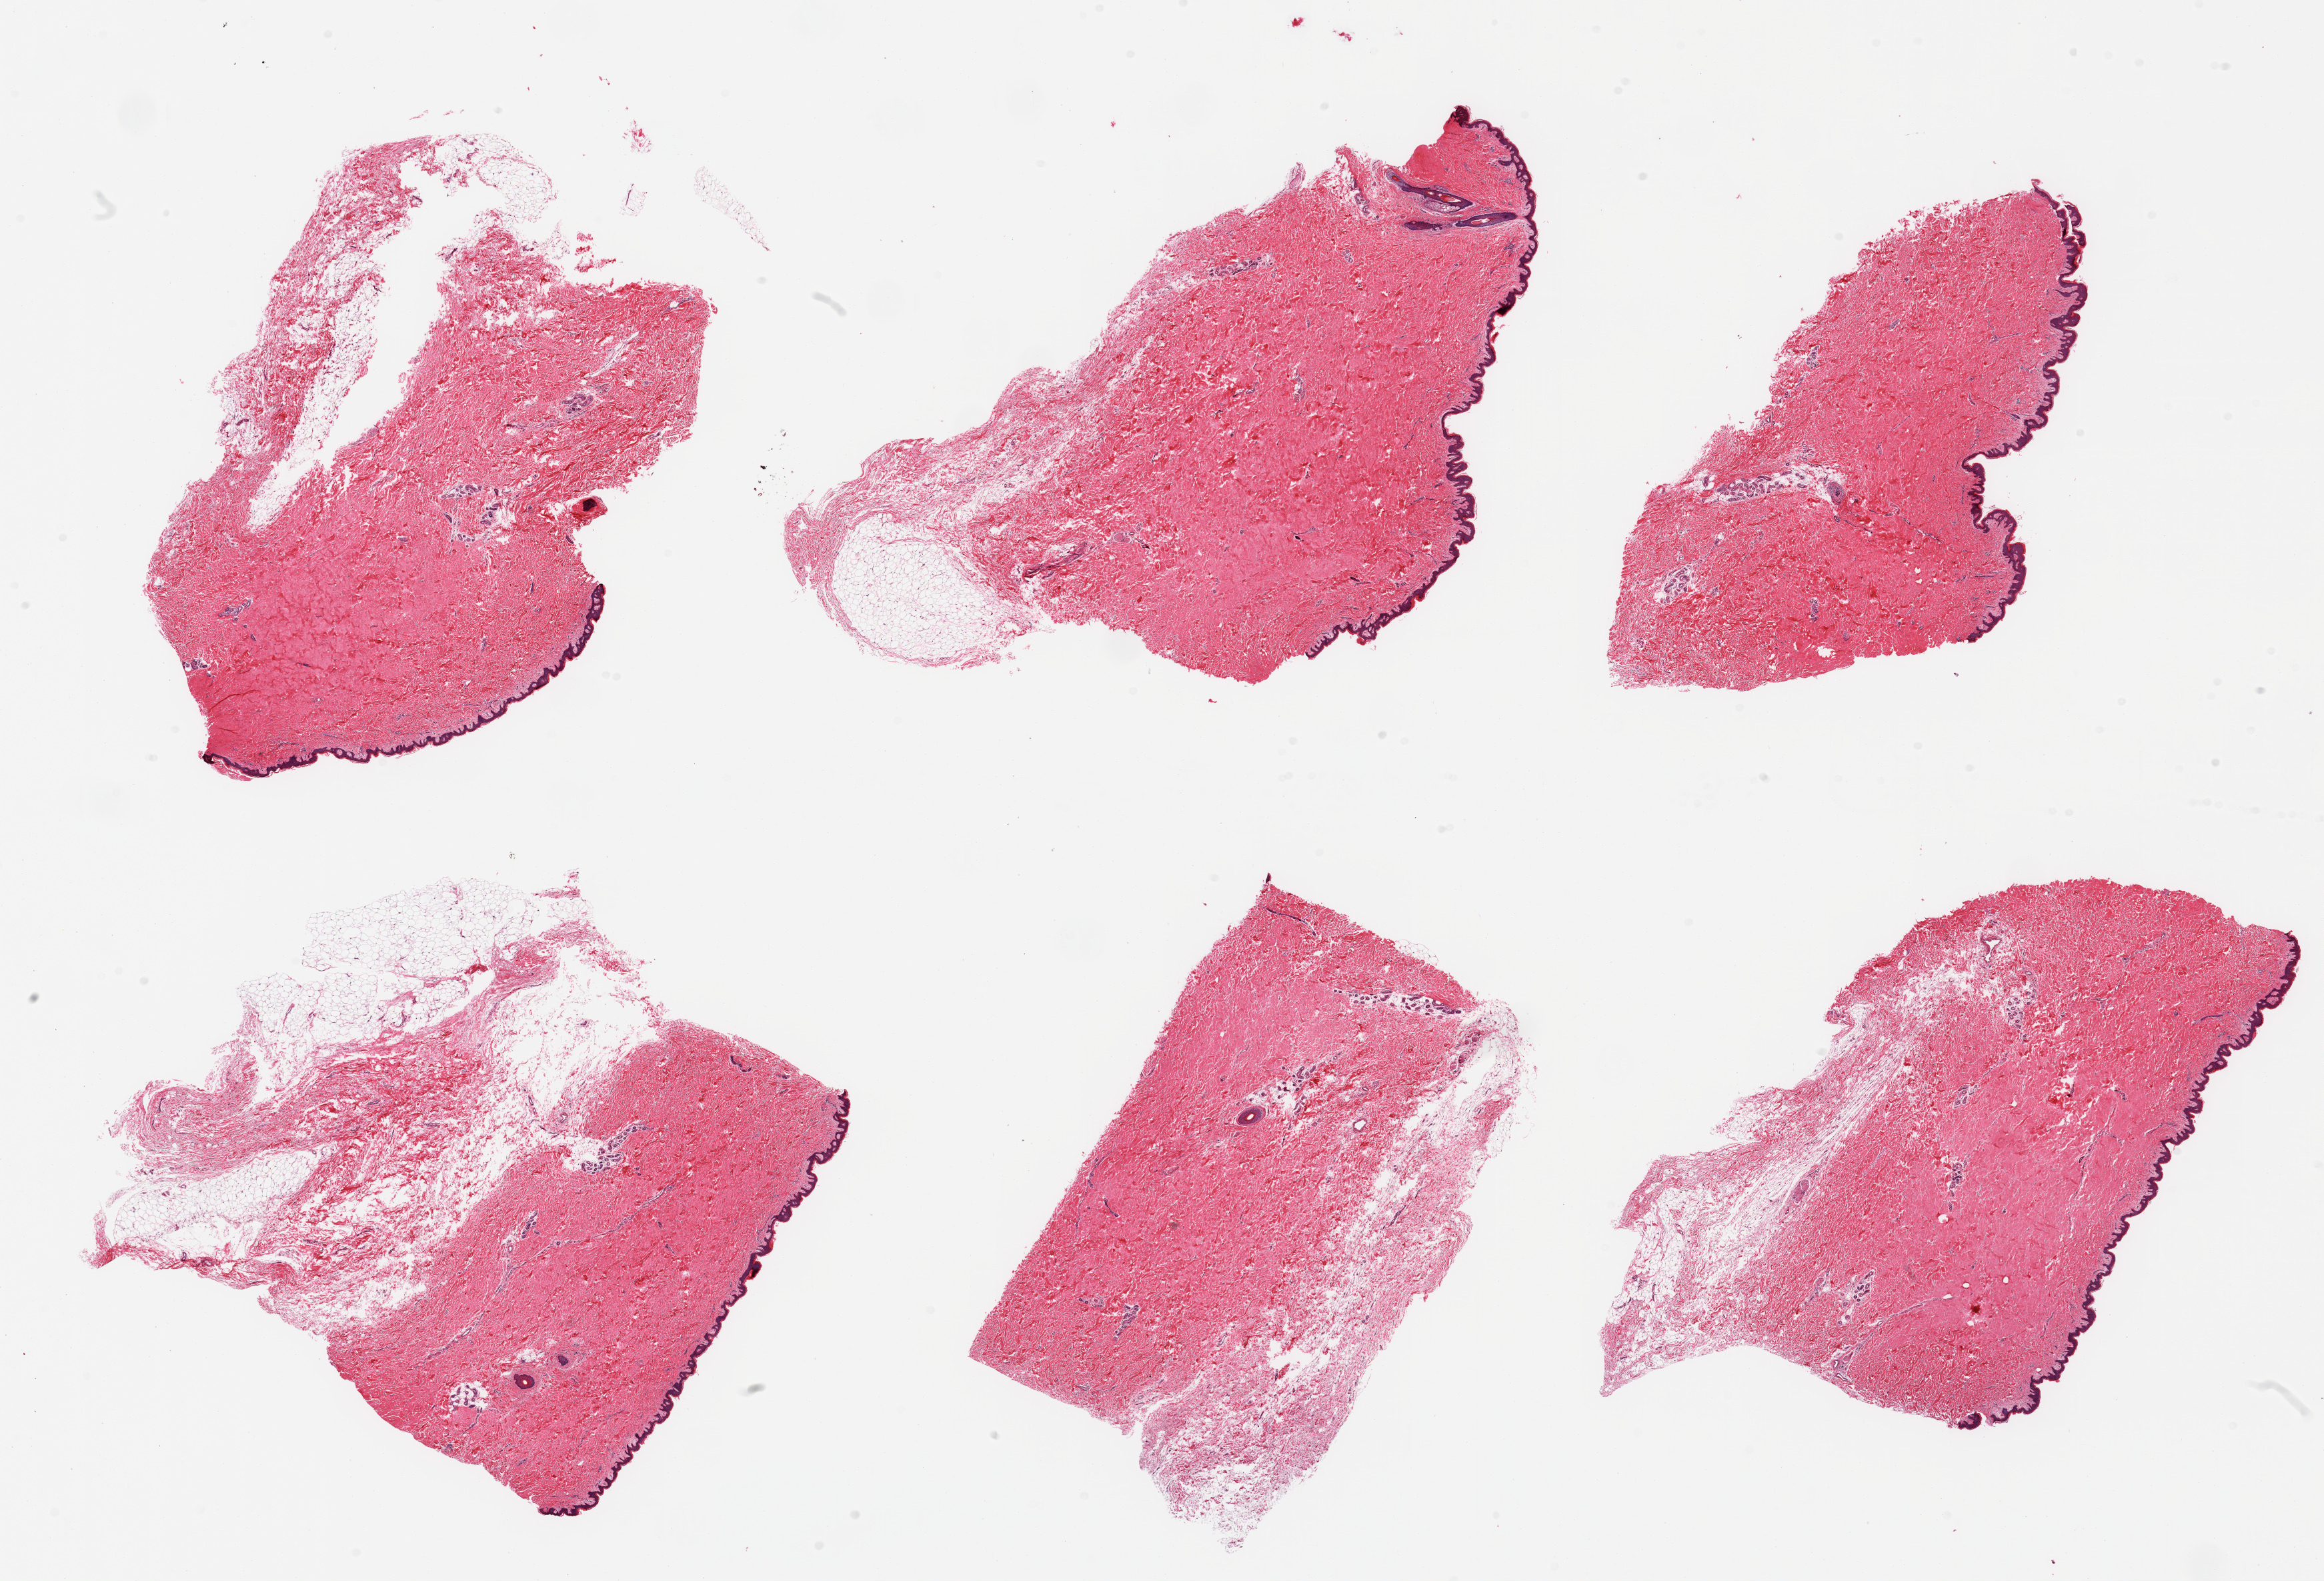
Digitized hematoxylin and eosin (H&E)-stained section, a low-resolution overview of the entire scanned area, about 27.6 x 18.8 mm (acquisition: 20x scan), PAXgene-fixed paraffin-embedded (PFPE) section, sampled site (target tissue): skin of lower leg, tissue donor sample.
Review note (as recorded): 6 pieces; few contain significant attached adipose tissue (up to 50%), one lacks epidermis in this section, elsewhere epidermis measures about 29 microns.